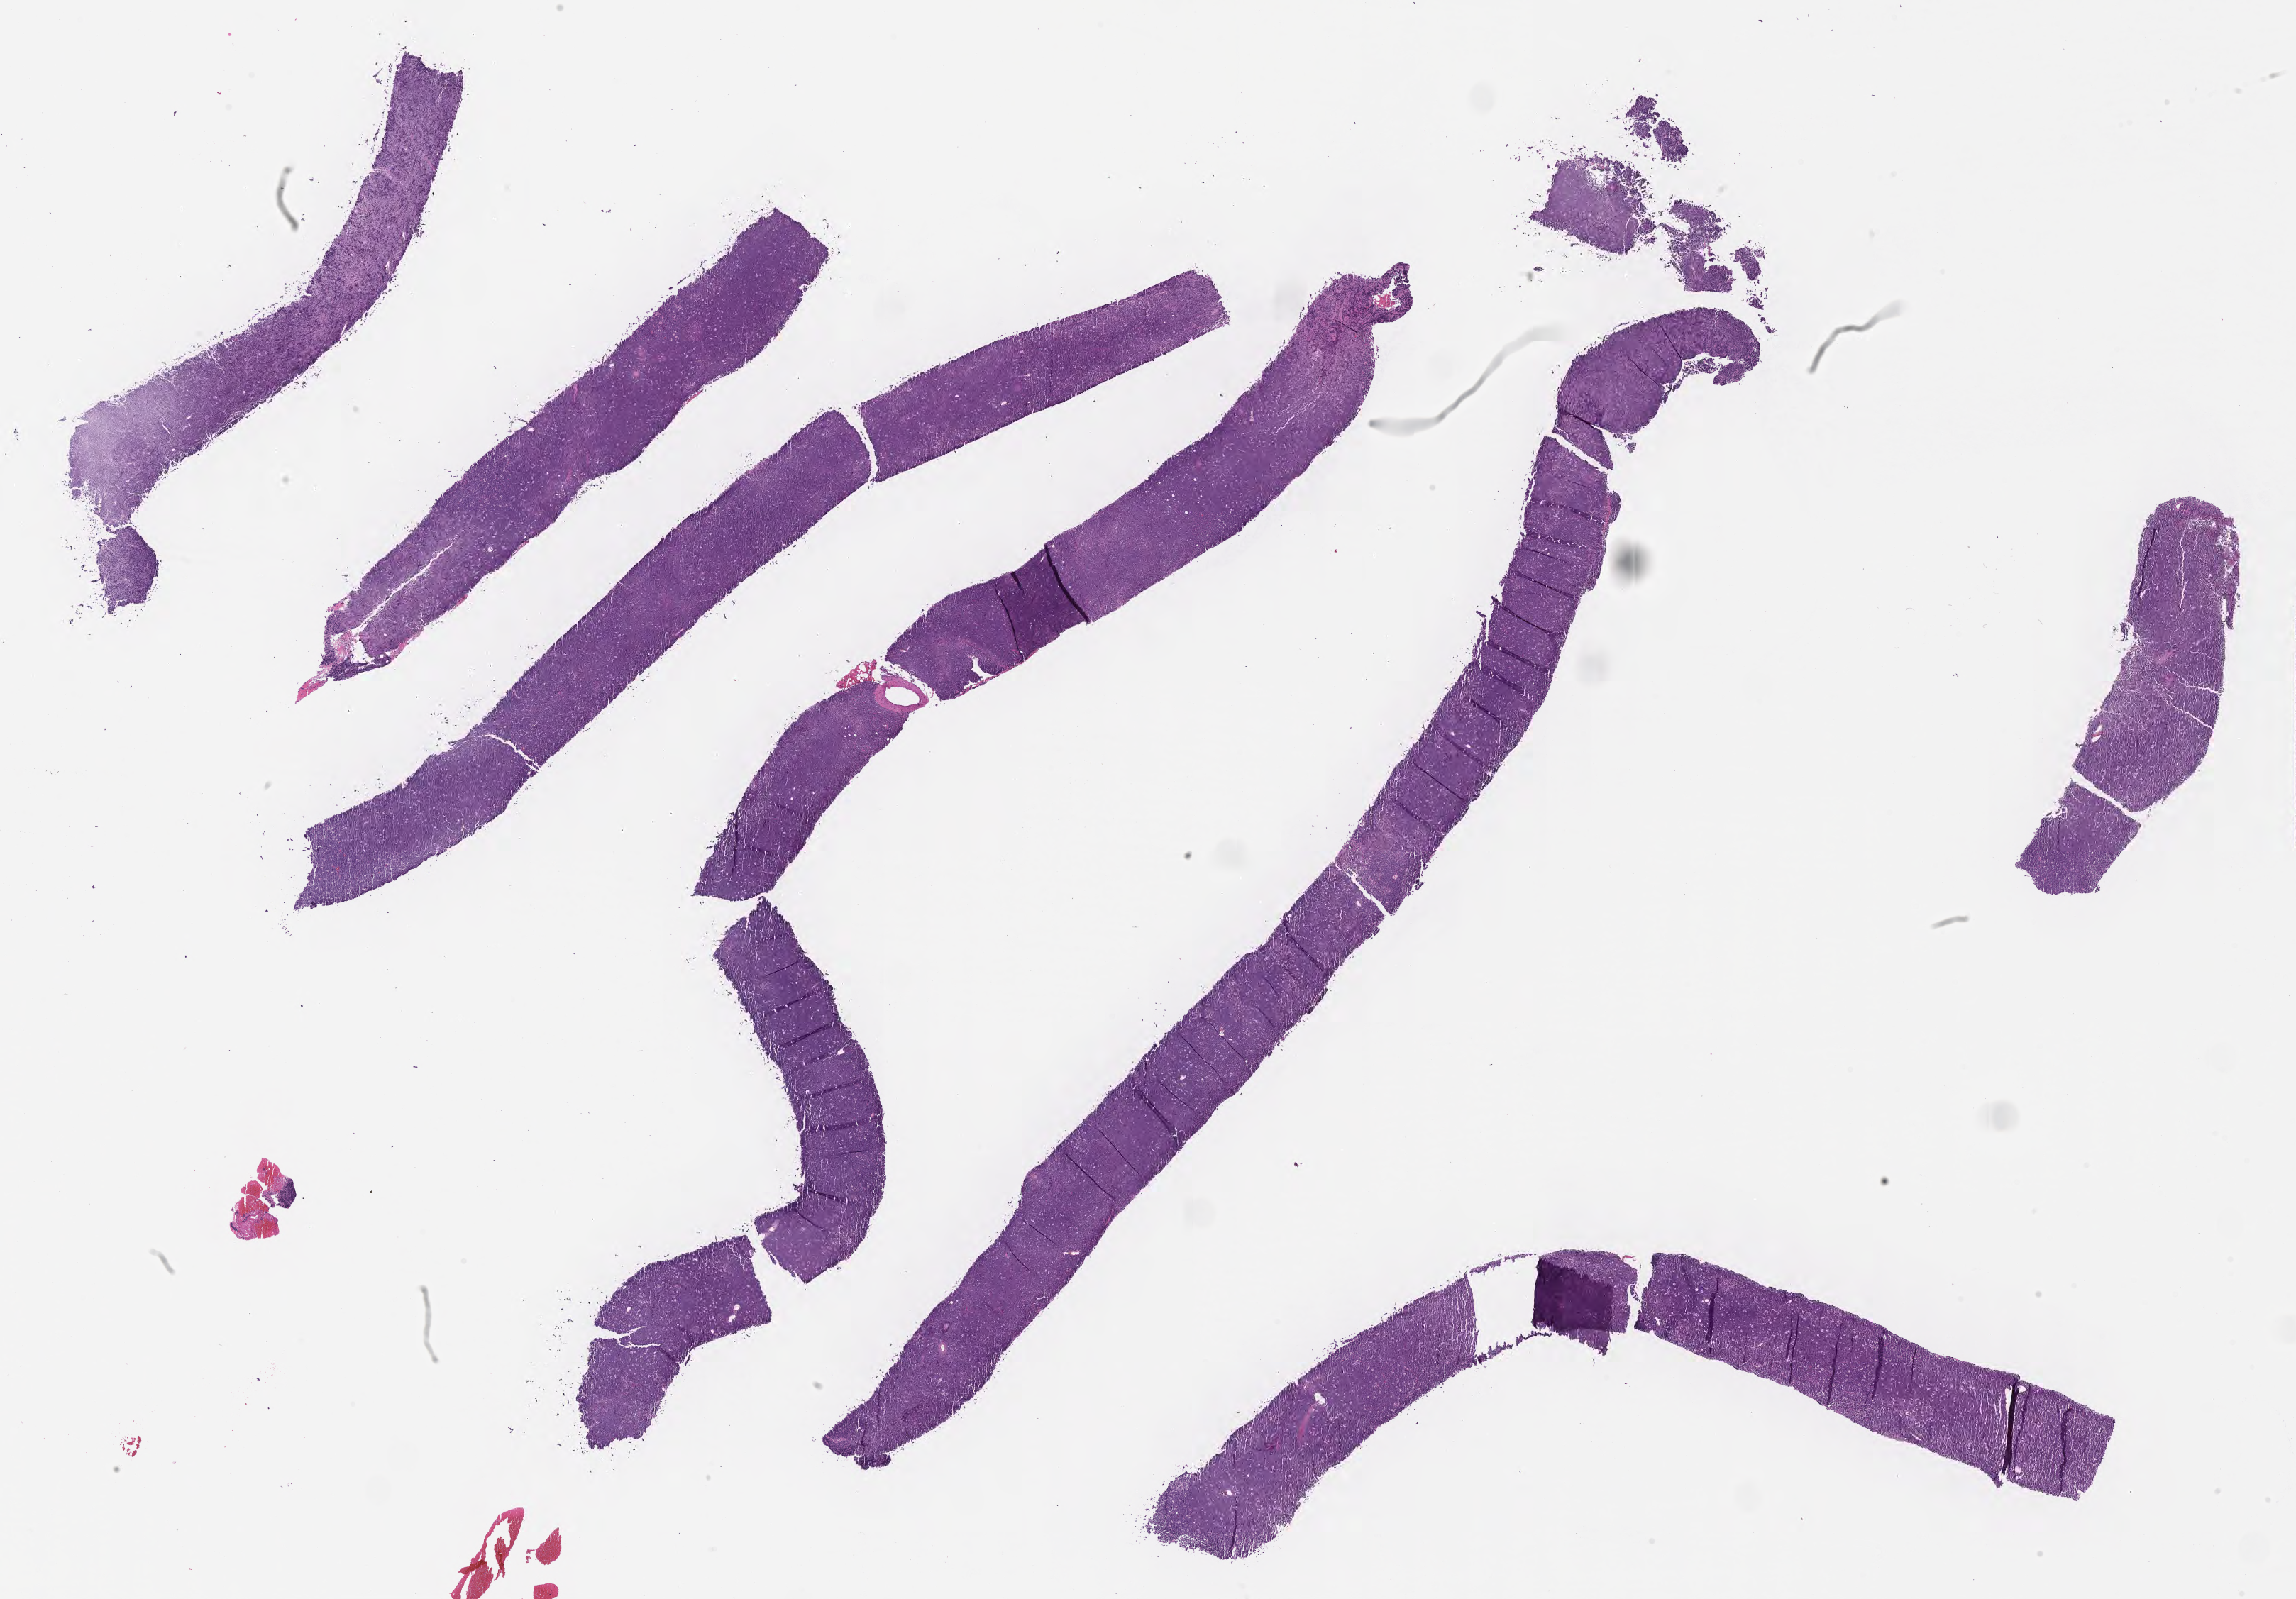
H&E whole-slide image — a low-resolution overview of the entire scanned area, about 26.2 x 18.2 mm. FFPE section. Primary tumor. Male patient, age 29 years. Pathologist review of this section (percent, as recorded): tumor cells 95%, tumor nuclei 95%.
Histologic diagnosis: Burkitt lymphoma, NOS.